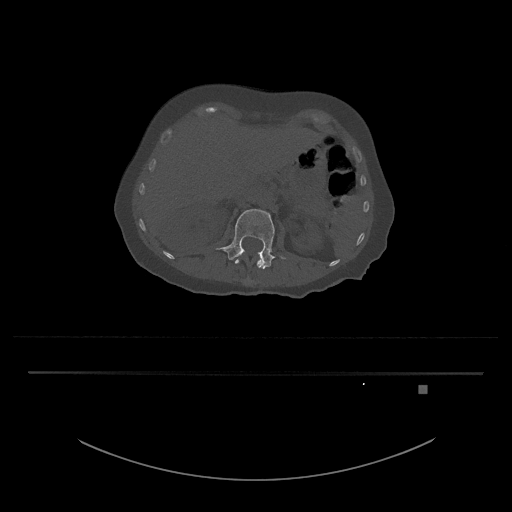
CT including the spine, one axial slice. Position 508 of 797 along the scan axis. 120 kVp. Bone window (W 1800 / L 400 HU). 0.5 mm slice thickness. 512 × 512 image matrix, field of view 500 × 500 mm. Female patient, age 57 years. Case-level facts recorded for this patient, not image findings: primary cancer: cervical.
Annotated regions visible in this slice (semi-automatic segmentation, software-assisted and operator-edited):
- L1 vertebra: bounding box (x1, y1, x2, y2) in pixels: (235, 250, 266, 268)